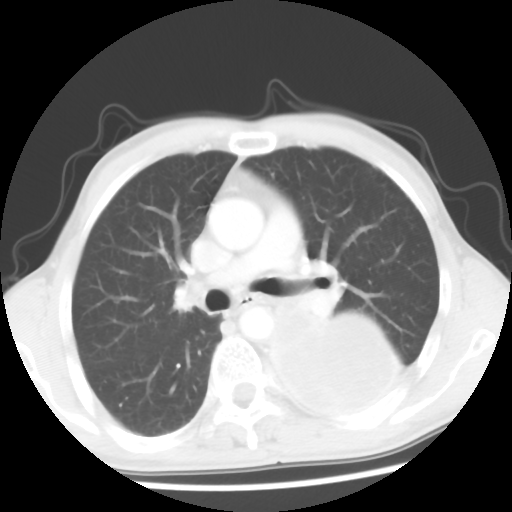
Chest CT, one axial slice; slice 35 of 56 in the series (ordered by position); 120 kVp; lung window (W 1500 / L -600 HU); 512 × 512 image matrix, field of view 318 × 318 mm. Male patient, age 60 years. From the clinical record (not read from this slice): clinical TNM (as recorded): T4 N0 M0.
Outlined on this slice (bounding box drawn by a radiologist):
- lung tumour (recorded histology: squamous cell carcinoma): bounding box (x1, y1, x2, y2) in pixels: (263, 294, 398, 418)